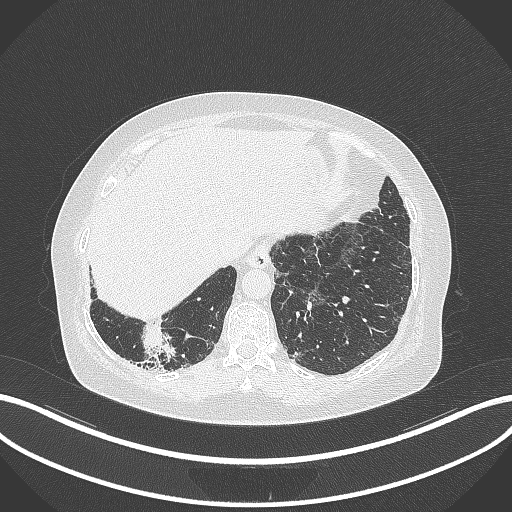
Chest CT, one axial slice; slice 24 of 296 in the series (ordered by position); reconstruction kernel B70f; lung window (W 1500 / L -600 HU); 512 × 512 image matrix, field of view 400 × 400 mm. Patient: female, 65 years. Case-level facts recorded for this patient, not image findings: clinical TNM (as recorded): T2b N1 M0.
Outlined on this slice (bounding box drawn by a radiologist):
- lung tumour (recorded histology: adenocarcinoma): bounding box [x1, y1, x2, y2] px = [137, 323, 178, 364]